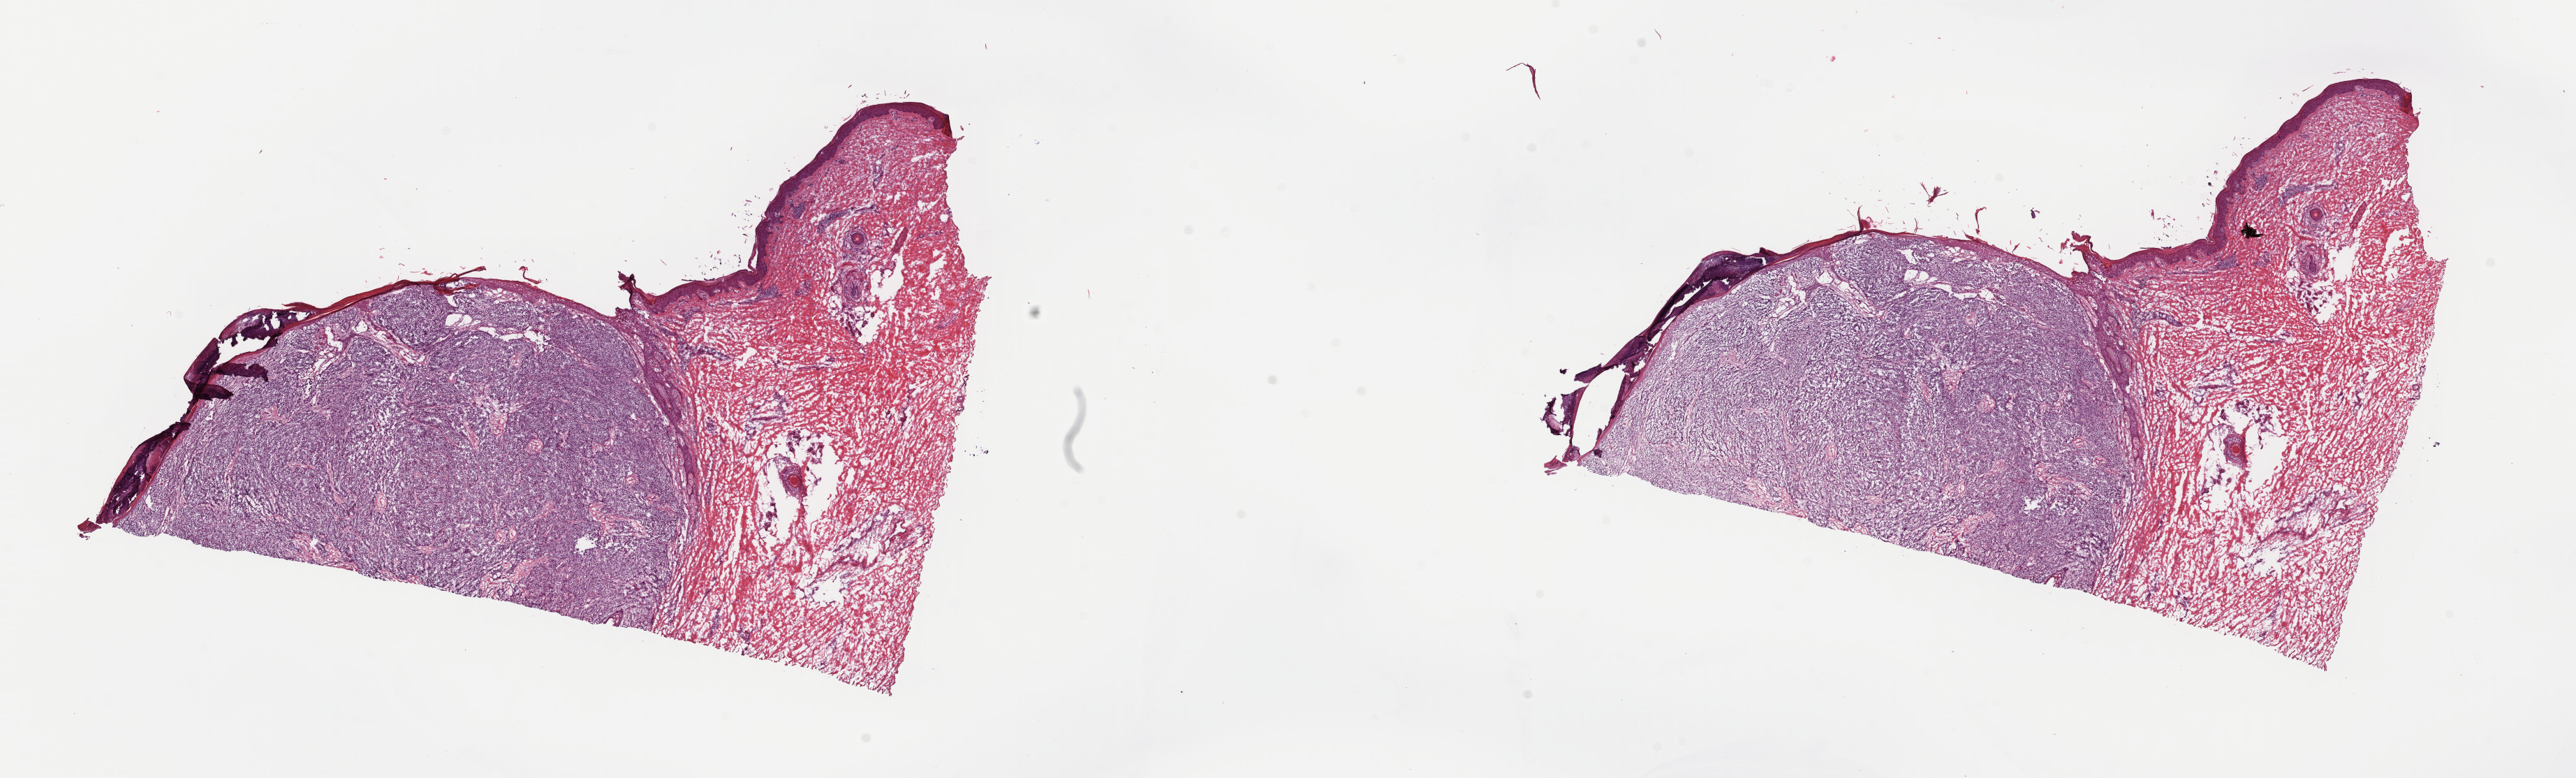
Digitized Hematoxylin and eosin (H&E) stained tissue section (whole slide), shown as a low-resolution overview of the whole scanned area (about 29.1 x 8.8 mm, acquisition: 40x scan); frozen section from the top of the tissue portion; sample: primary tumour, skin. Female, age 56 years at initial diagnosis.
Pathologic diagnosis: Nodular melanoma.